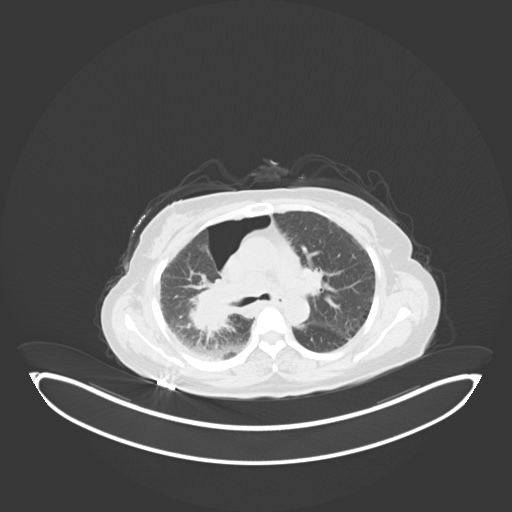
Chest CT, one axial slice. Slice 37 of 69 in the series (ordered by position). Lung window (W 1500 / L -600 HU). 512 × 512 image matrix. Patient: female, 64 years. From the clinical record (not read from this slice): clinical TNM (as recorded): T3 N3 M0.
Outlined on this slice (rectangle marked by the reading radiologist):
- lung tumour (recorded histology: squamous cell carcinoma): bounding box <176,276,238,339> (left, top, right, bottom; pixels)